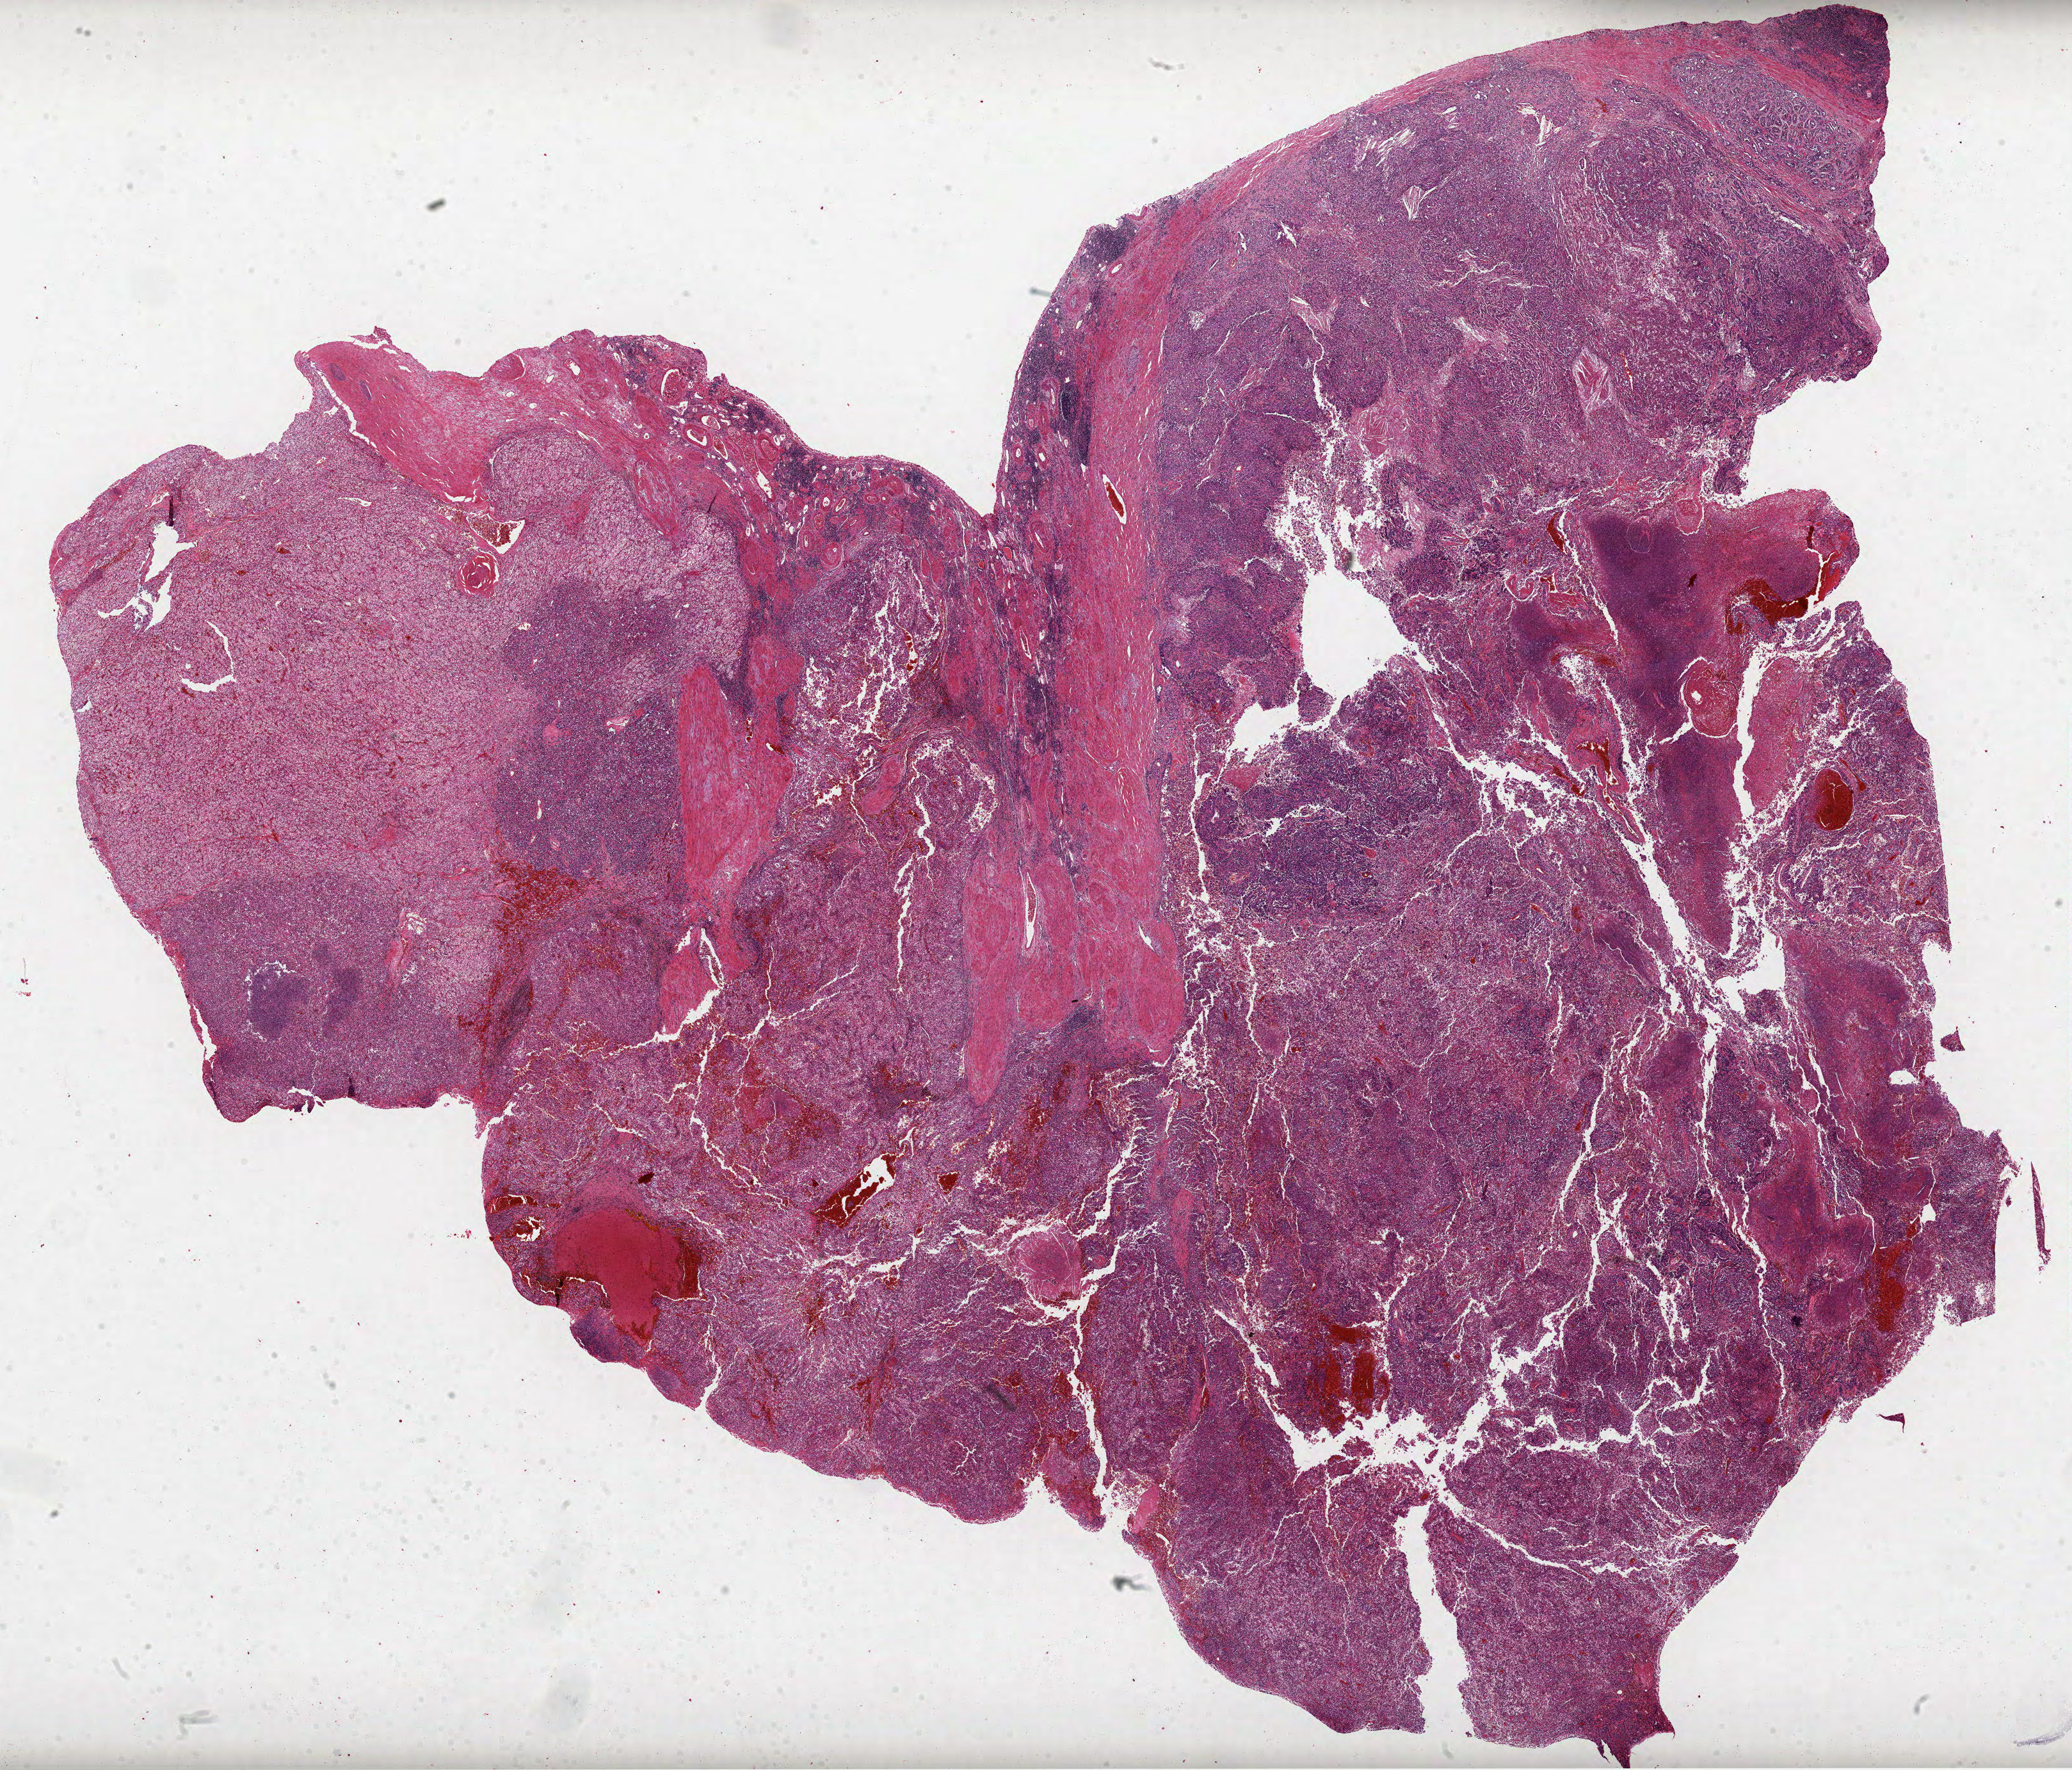
Digitized H&E-stained tissue section (whole slide), a low-resolution overview of the entire scanned area, about 26.1 x 22.3 mm (acquisition: 40x scan). Formalin-fixed paraffin-embedded (FFPE) diagnostic section. Kidney, primary tumour sample. Female patient; age at initial diagnosis 66 years. Histologic grade: G3 (poorly differentiated).
Lymph nodes positive (case pathology): 0 of 1 examined. Laterality: left. Pathologic diagnosis: Clear cell adenocarcinoma, NOS. AJCC pathologic stage: IV.